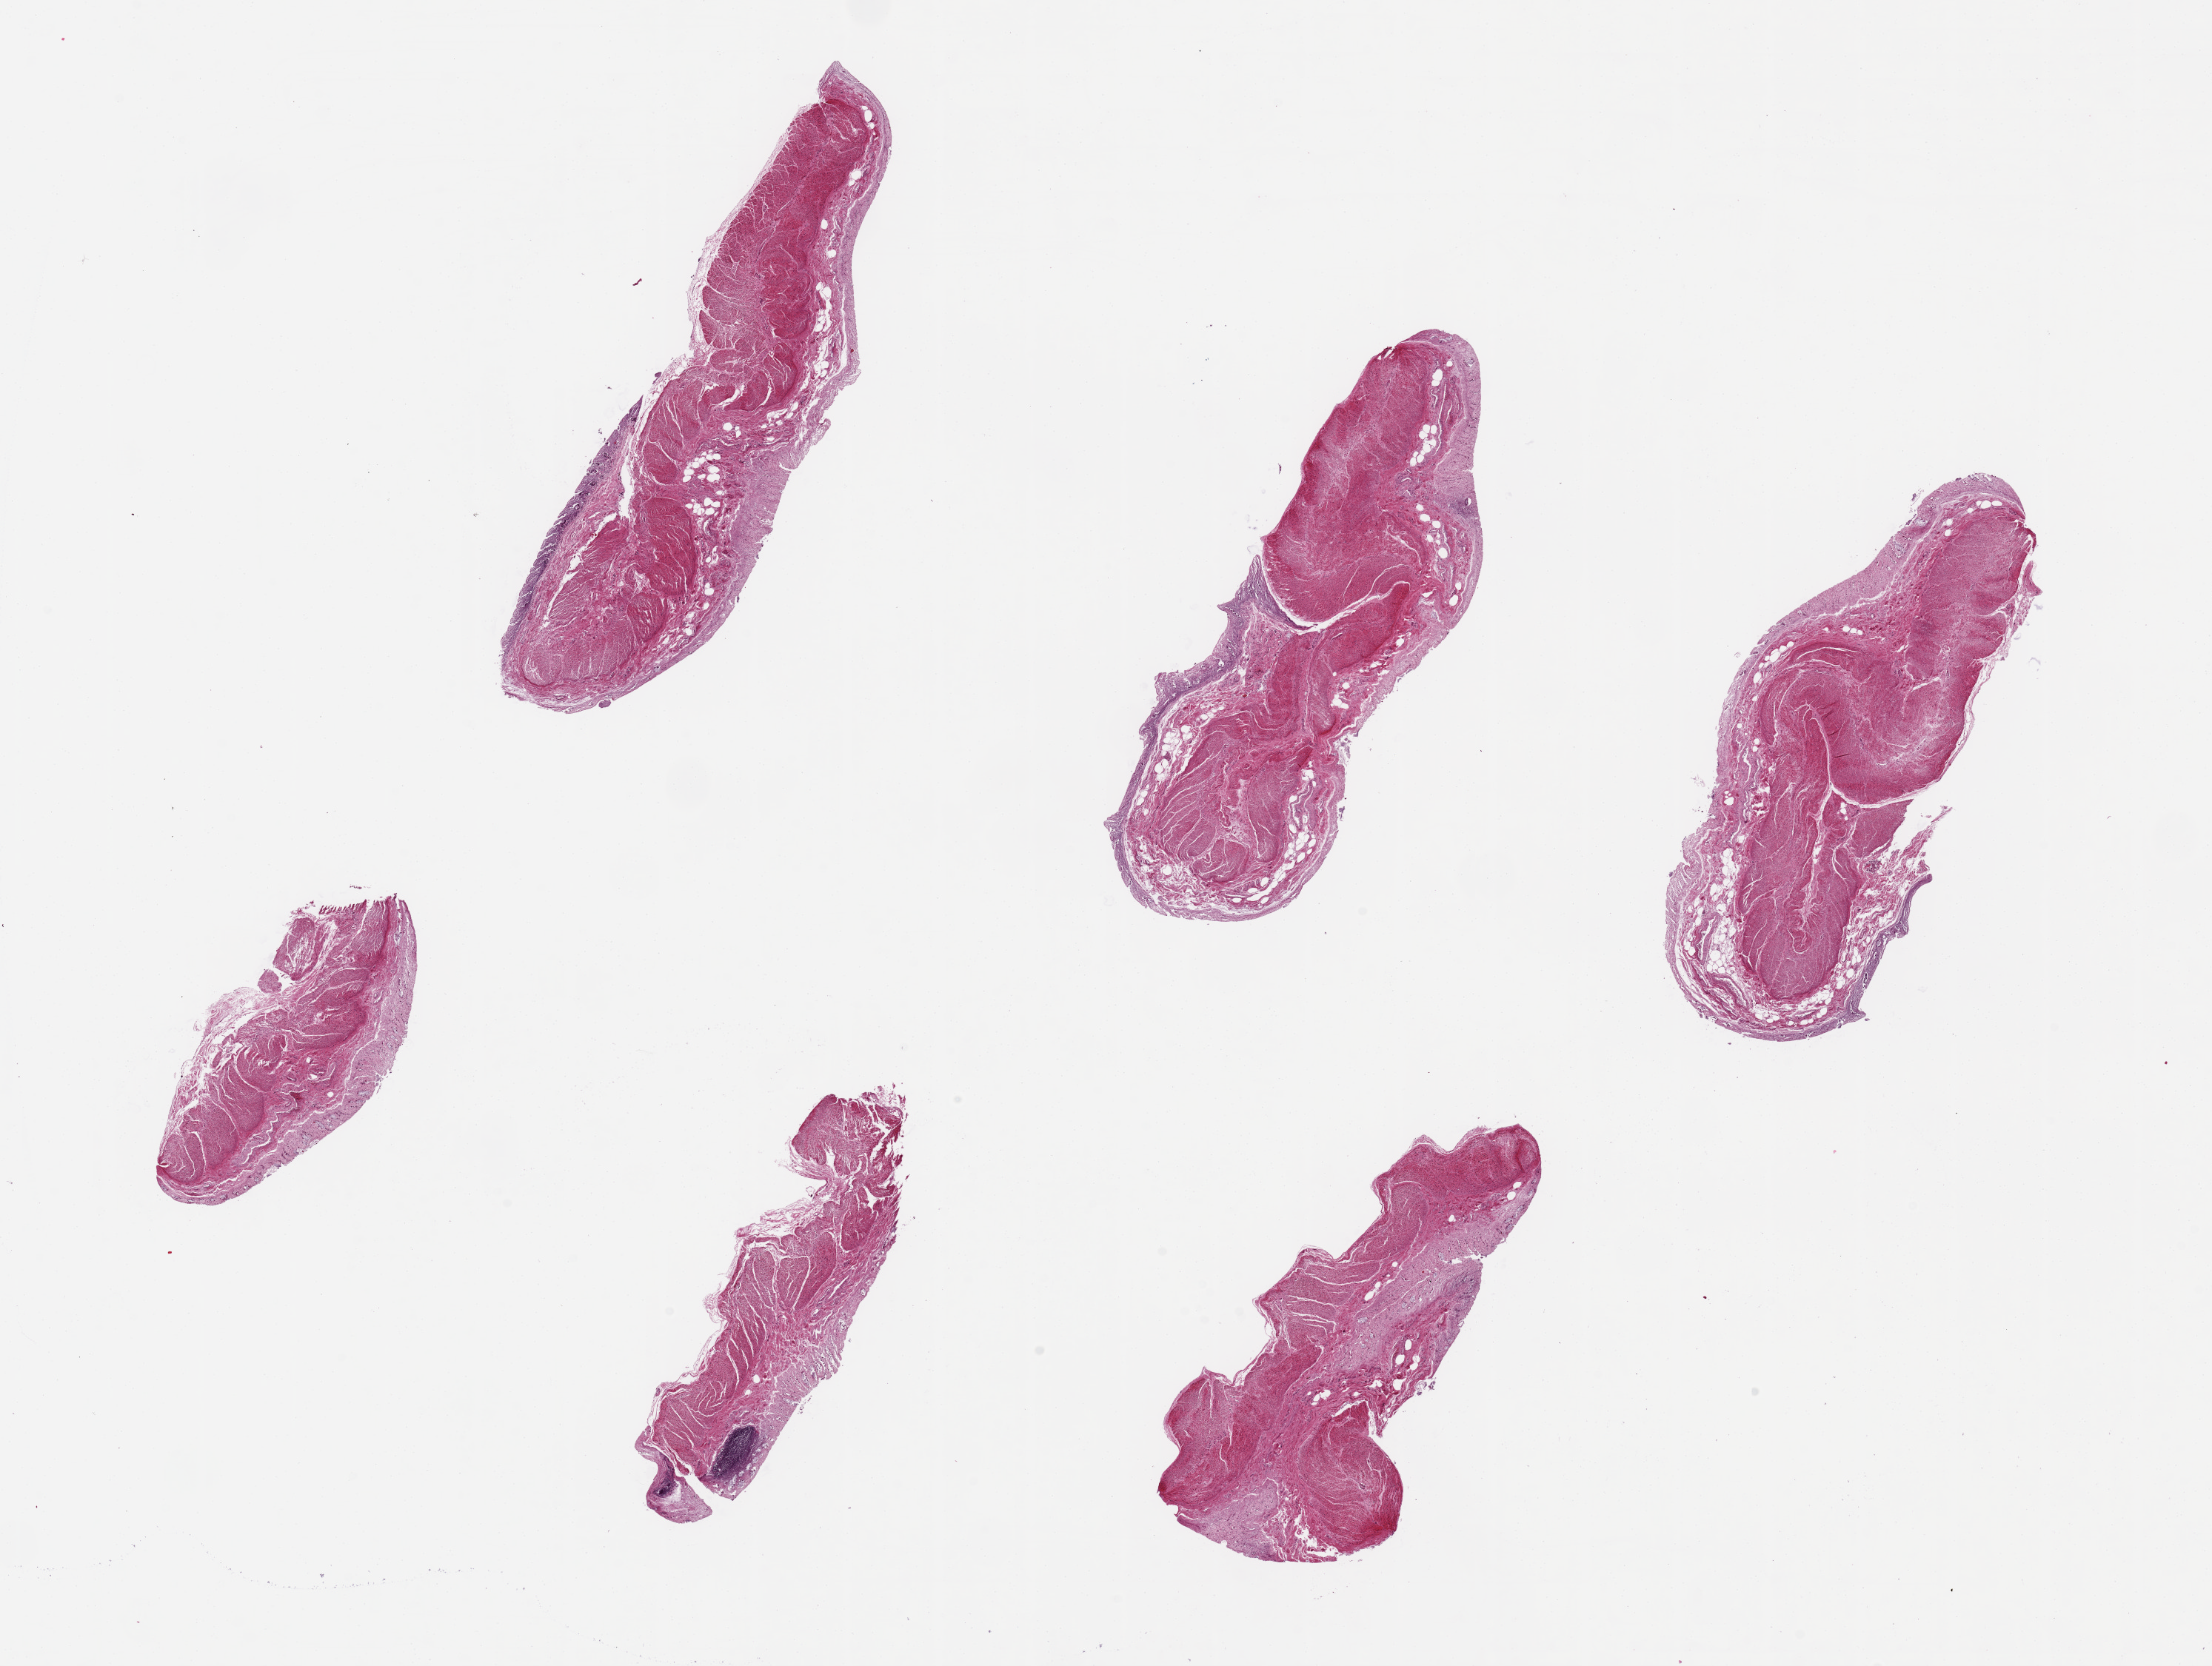
Hematoxylin and eosin (H&E) whole-slide image, shown as a low-resolution overview of the whole scanned area (about 23.6 x 17.8 mm, from a 20x scan), PAXgene-fixed, paraffin-embedded tissue, sampled site (target tissue): transverse colon, tissue donor sample.
Pathologist's review note for this sample: 6 pieces, 7x2mm. Mucosa totally autolyzed.